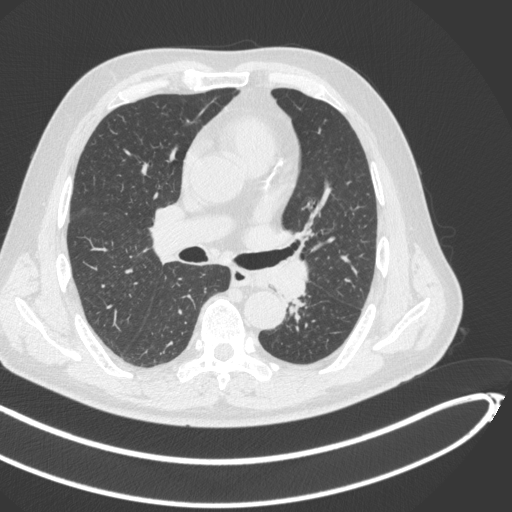
Chest CT, one axial slice. Slice 265 of 466 in the series (ordered by position). Lung window (W 1500 / L -600 HU). 512 × 512 image matrix, field of view 400 × 400 mm. Male patient, age 64 years. Case-level facts recorded for this patient, not image findings: clinical TNM (as recorded): T1c N0 M0; histopathological grade: G2.
Structures marked on this image (bounding box drawn by a radiologist):
- lung tumour (recorded histology: squamous cell carcinoma): box from (x=250, y=263) to (x=313, y=304) px